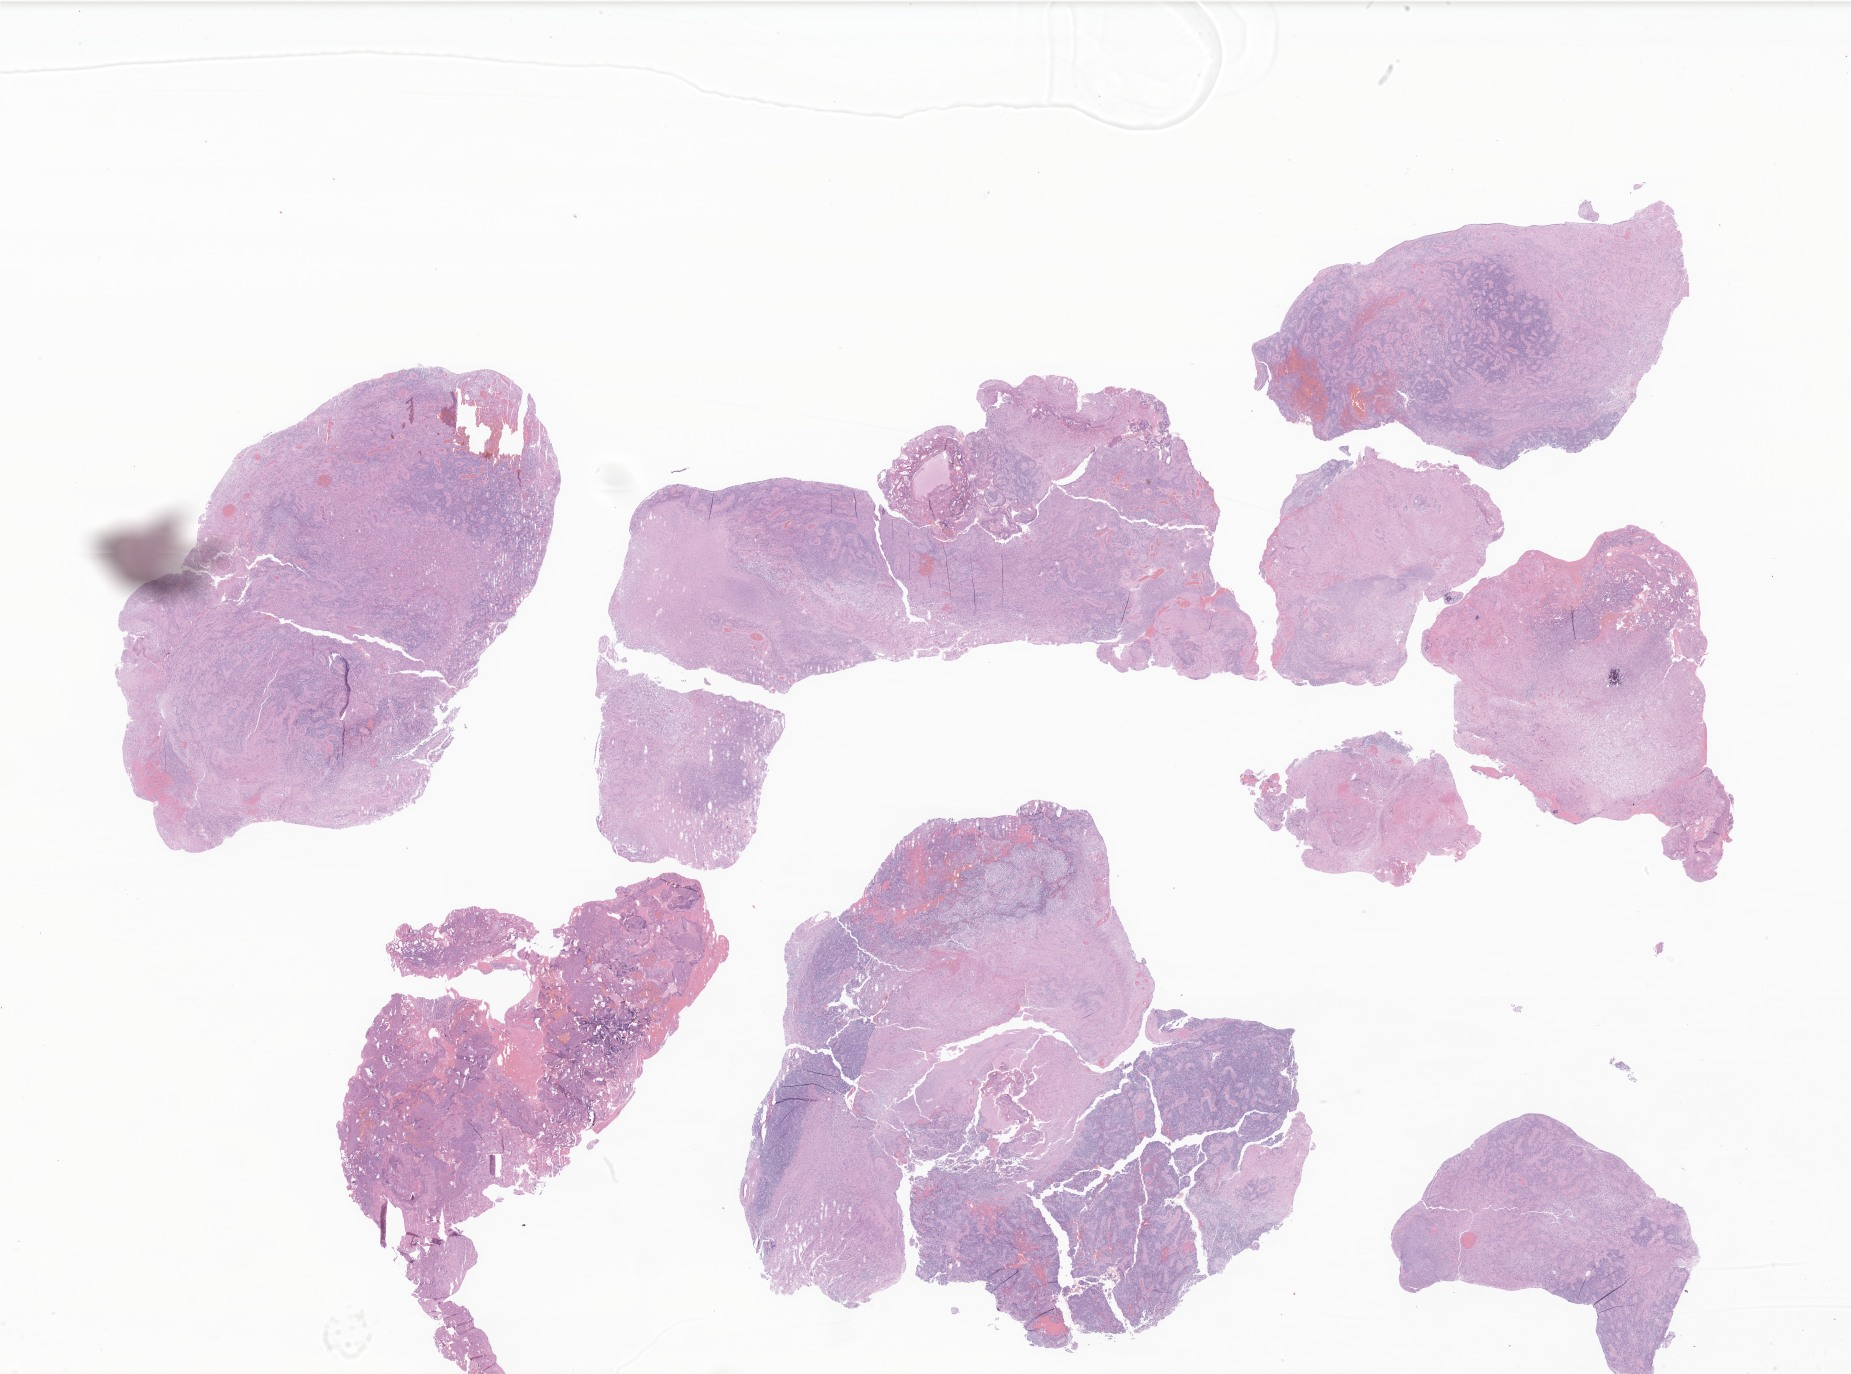
Digitized hematoxylin and eosin (H&E)-stained section of tumor tissue from the brain — whole scanned area (about 31.2 x 23.2 mm) shown as a low-resolution overview, formalin-fixed, paraffin-embedded (FFPE) tissue. Patient: female, age 437 days (about 1.2 years).
Diagnosis (ICD-O-3 morphology term): Ependymoma, NOS.